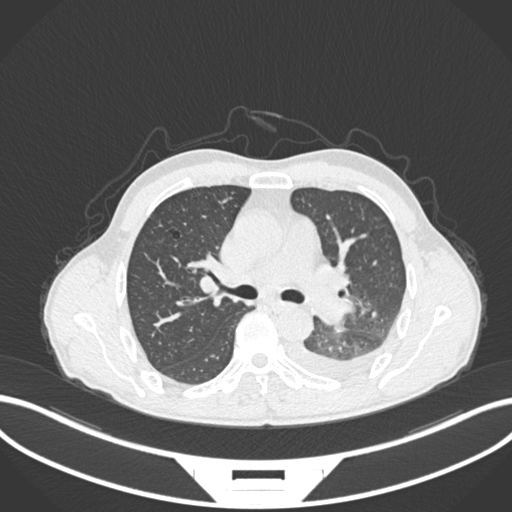
Chest CT, one axial slice. Position 155 of 222 along the scan axis. Reconstruction kernel B30f. 120 kVp. Lung window (W 1500 / L -600 HU). 1 mm slice thickness. 512 × 512 image matrix, field of view 400 × 400 mm. Male patient, age 47 years. From the clinical record (not read from this slice): clinical TNM (as recorded): T3 N1 M1c.
Outlined on this slice (rectangle marked by the reading radiologist):
- lung tumour (recorded histology: small cell carcinoma): bounding box (x1, y1, x2, y2) in pixels: (316, 295, 358, 325)